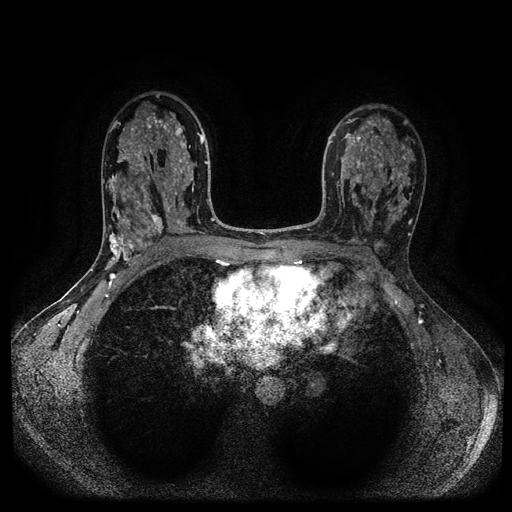
Breast MRI (dynamic contrast-enhanced, multi-phase), one axial slice. Slice 63 of 116 in the series (ordered by position). Dynamic contrast-enhanced series, time point 2 of 5 at this slice position (early post-contrast). 1.5 T. TE 2.6 ms, TR 5.4 ms. 2 mm slice thickness. 512 × 512 image matrix, field of view 340 × 340 mm. Female patient, age 43 years.
Outlined on this slice (semi-automatically segmented with operator editing):
- breast lesion (labelled benign in the annotation): bounding box <148,210,164,235> (left, top, right, bottom; pixels)